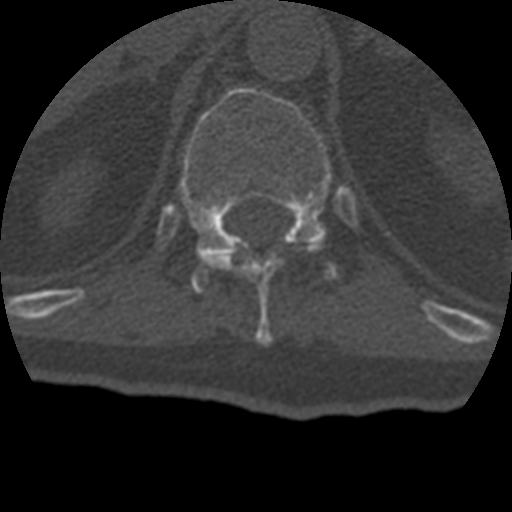
CT including the spine, one axial slice; slice 183 of 399 in the series (ordered by position); 120 kVp; bone window (W 1800 / L 400 HU); 1.25 mm slice thickness; 512 × 512 image matrix, field of view 160 × 160 mm. Patient age 69 years. From the clinical record (not read from this slice): primary cancer: prostate.
Annotated regions visible in this slice (semi-automatic segmentation, software-assisted and operator-edited):
- T11 vertebra: bounding box <208,239,327,345> (left, top, right, bottom; pixels)
- T12 vertebra: <180,87,338,289>